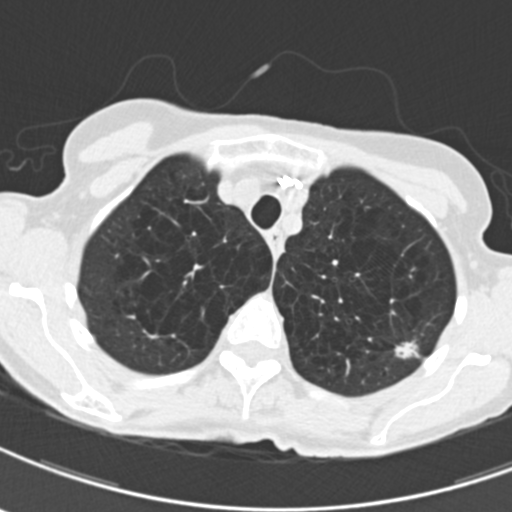
Low-dose screening chest CT, axial slice. Third screening round (two years after baseline). Lung window (W 1500 / L -600 HU). 2 mm slice thickness. 120 kVp. 512 × 512 image matrix. Female, age 71 years at enrolment. Current smoker at enrolment.
Expert reader's lesion annotation, bounding box [x1, y1, x2, y2] px = [388, 328, 433, 369]. The exam's reader record, not a measurement of the box and not confirmed to be the same lesion: non-calcified nodule or mass ≥4 mm, left upper lobe, 12 × 9 mm, spiculated (stellate) margins, mixed attenuation, pre-existing on the prior screen: yes; interval growth: yes. Official screen result: positive, other.